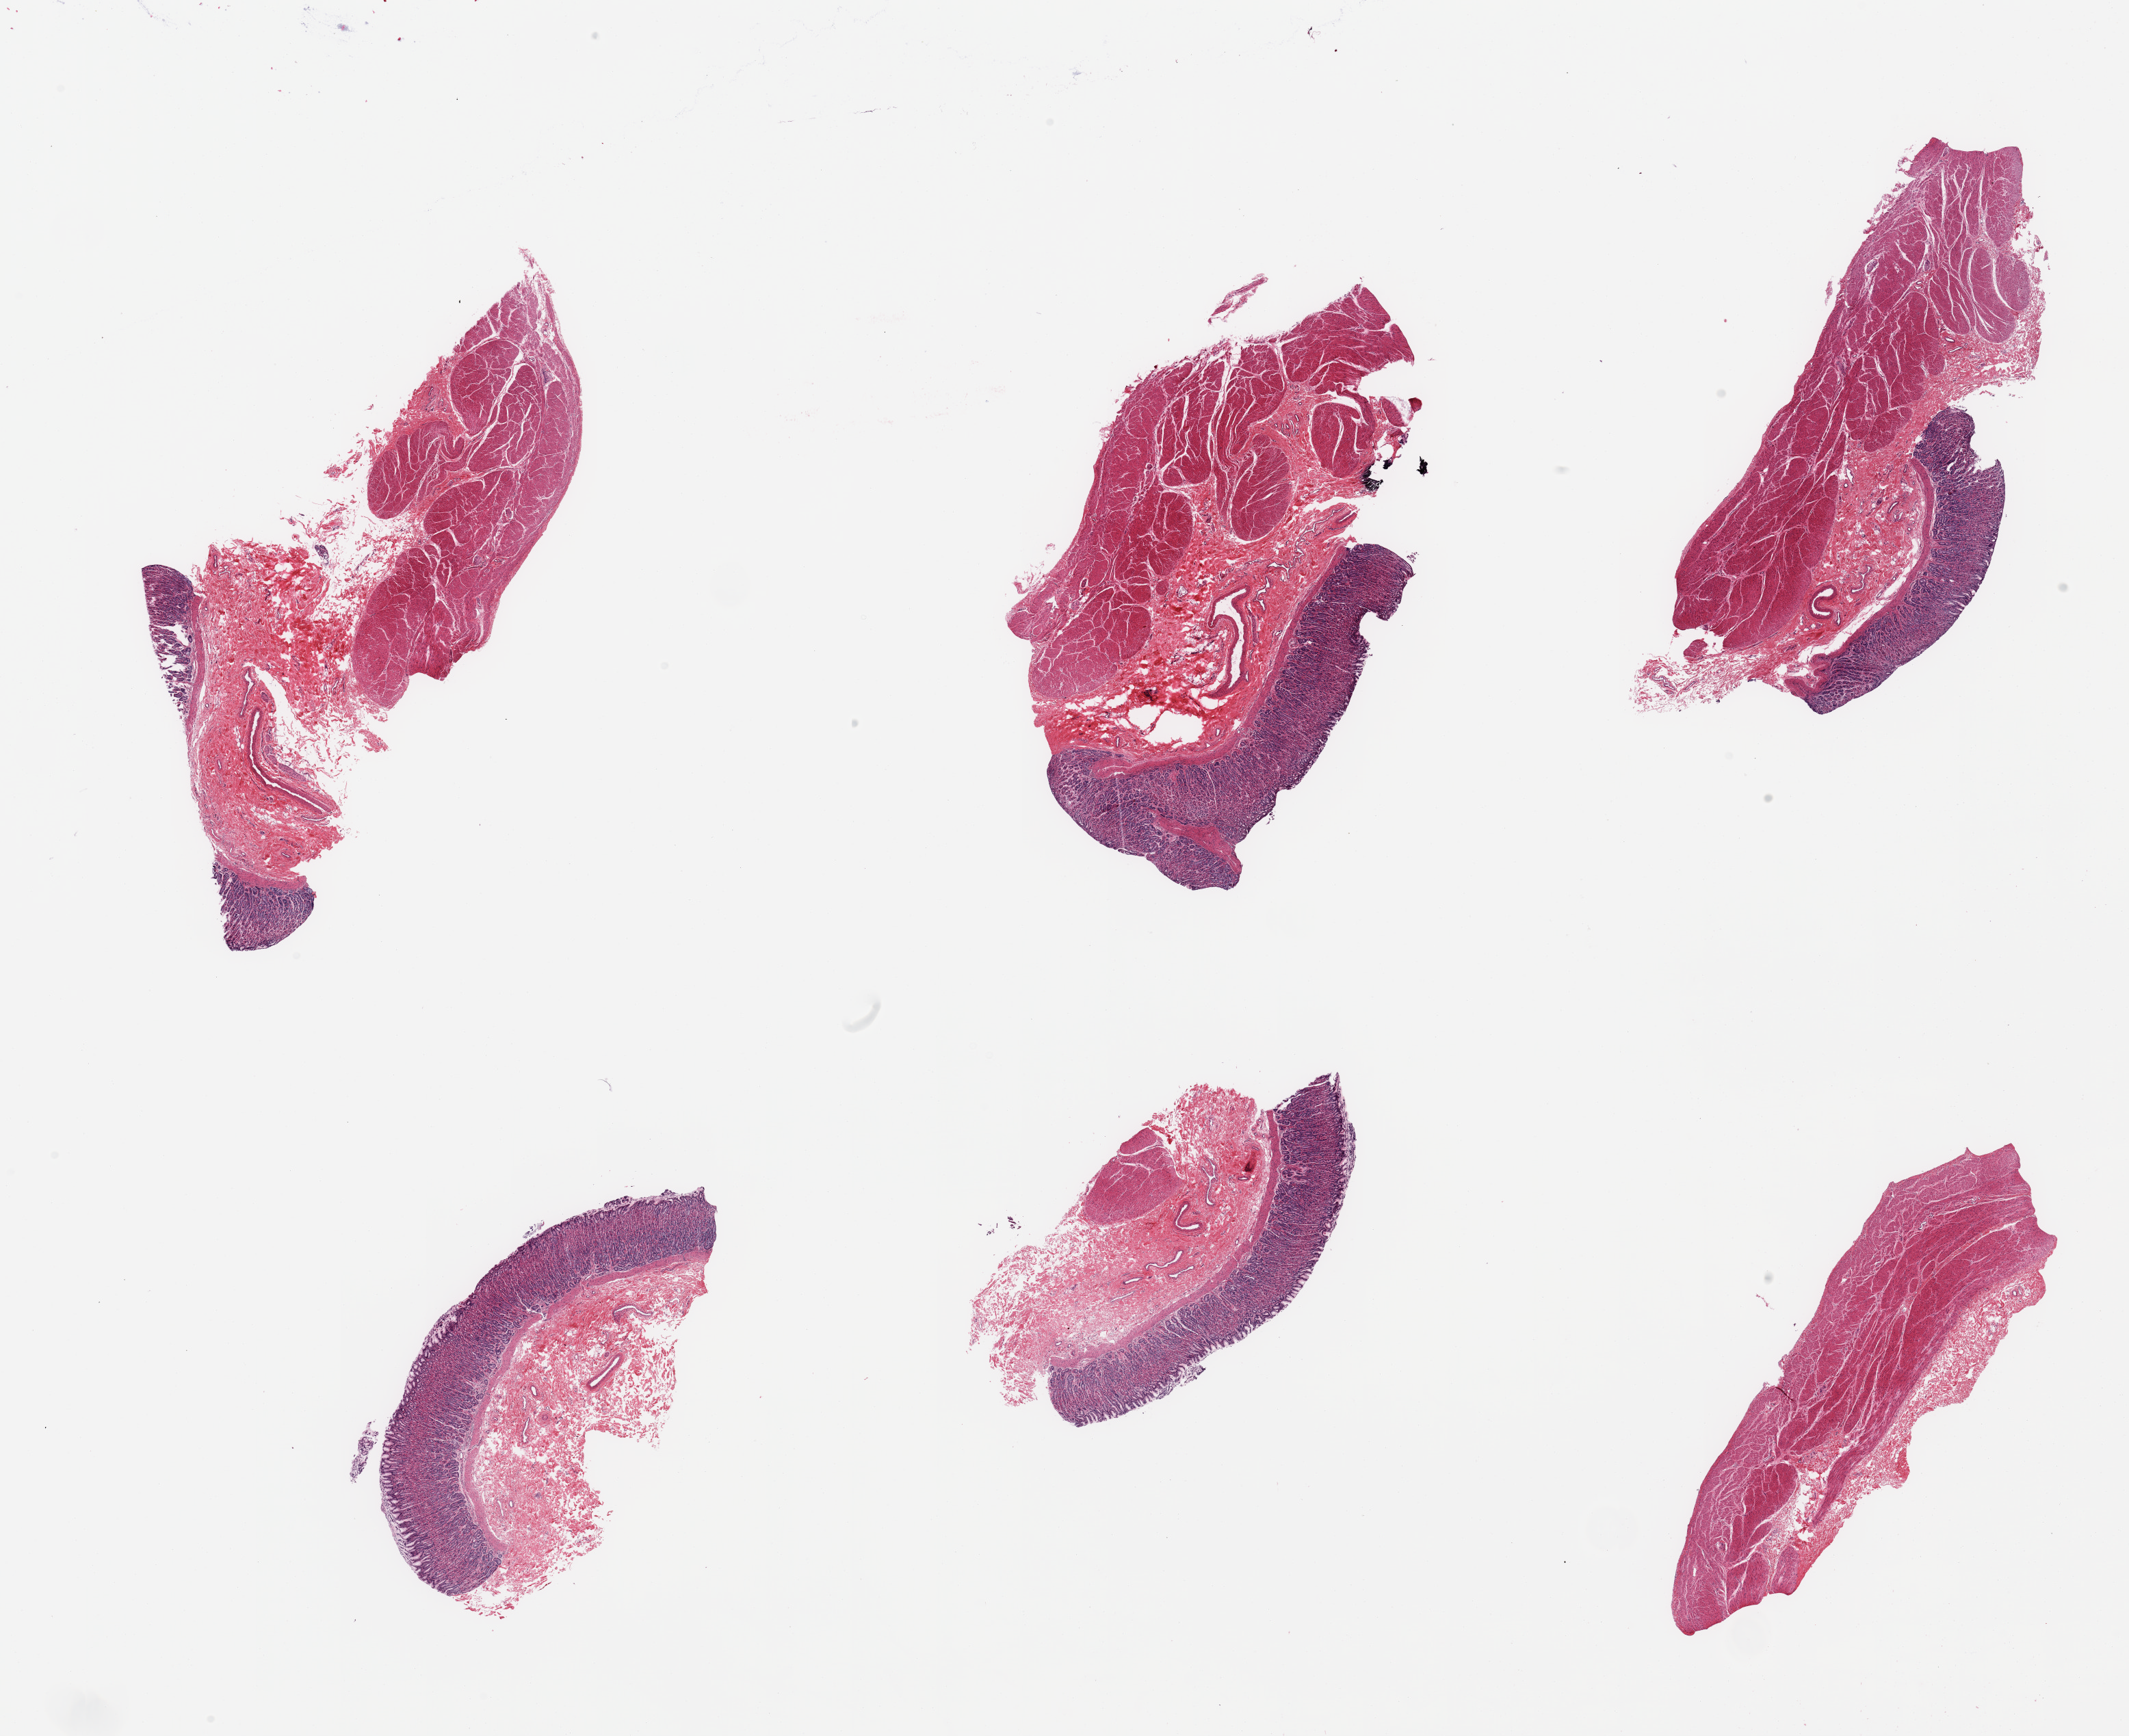
Whole-slide image, H&E stain — a low-resolution overview of the entire scanned area, about 24.6 x 20.1 mm (acquisition: 20x scan); PAXgene-fixed, paraffin-embedded tissue; sampled site (target tissue): stomach; tissue donor sample. Donor sex: female.
Review note (as recorded): 6 pieces; 3 full thickness, 1 mucosa only, 1 mostly muscle, 1 all muscle; mucosa, where present, very well preserved.